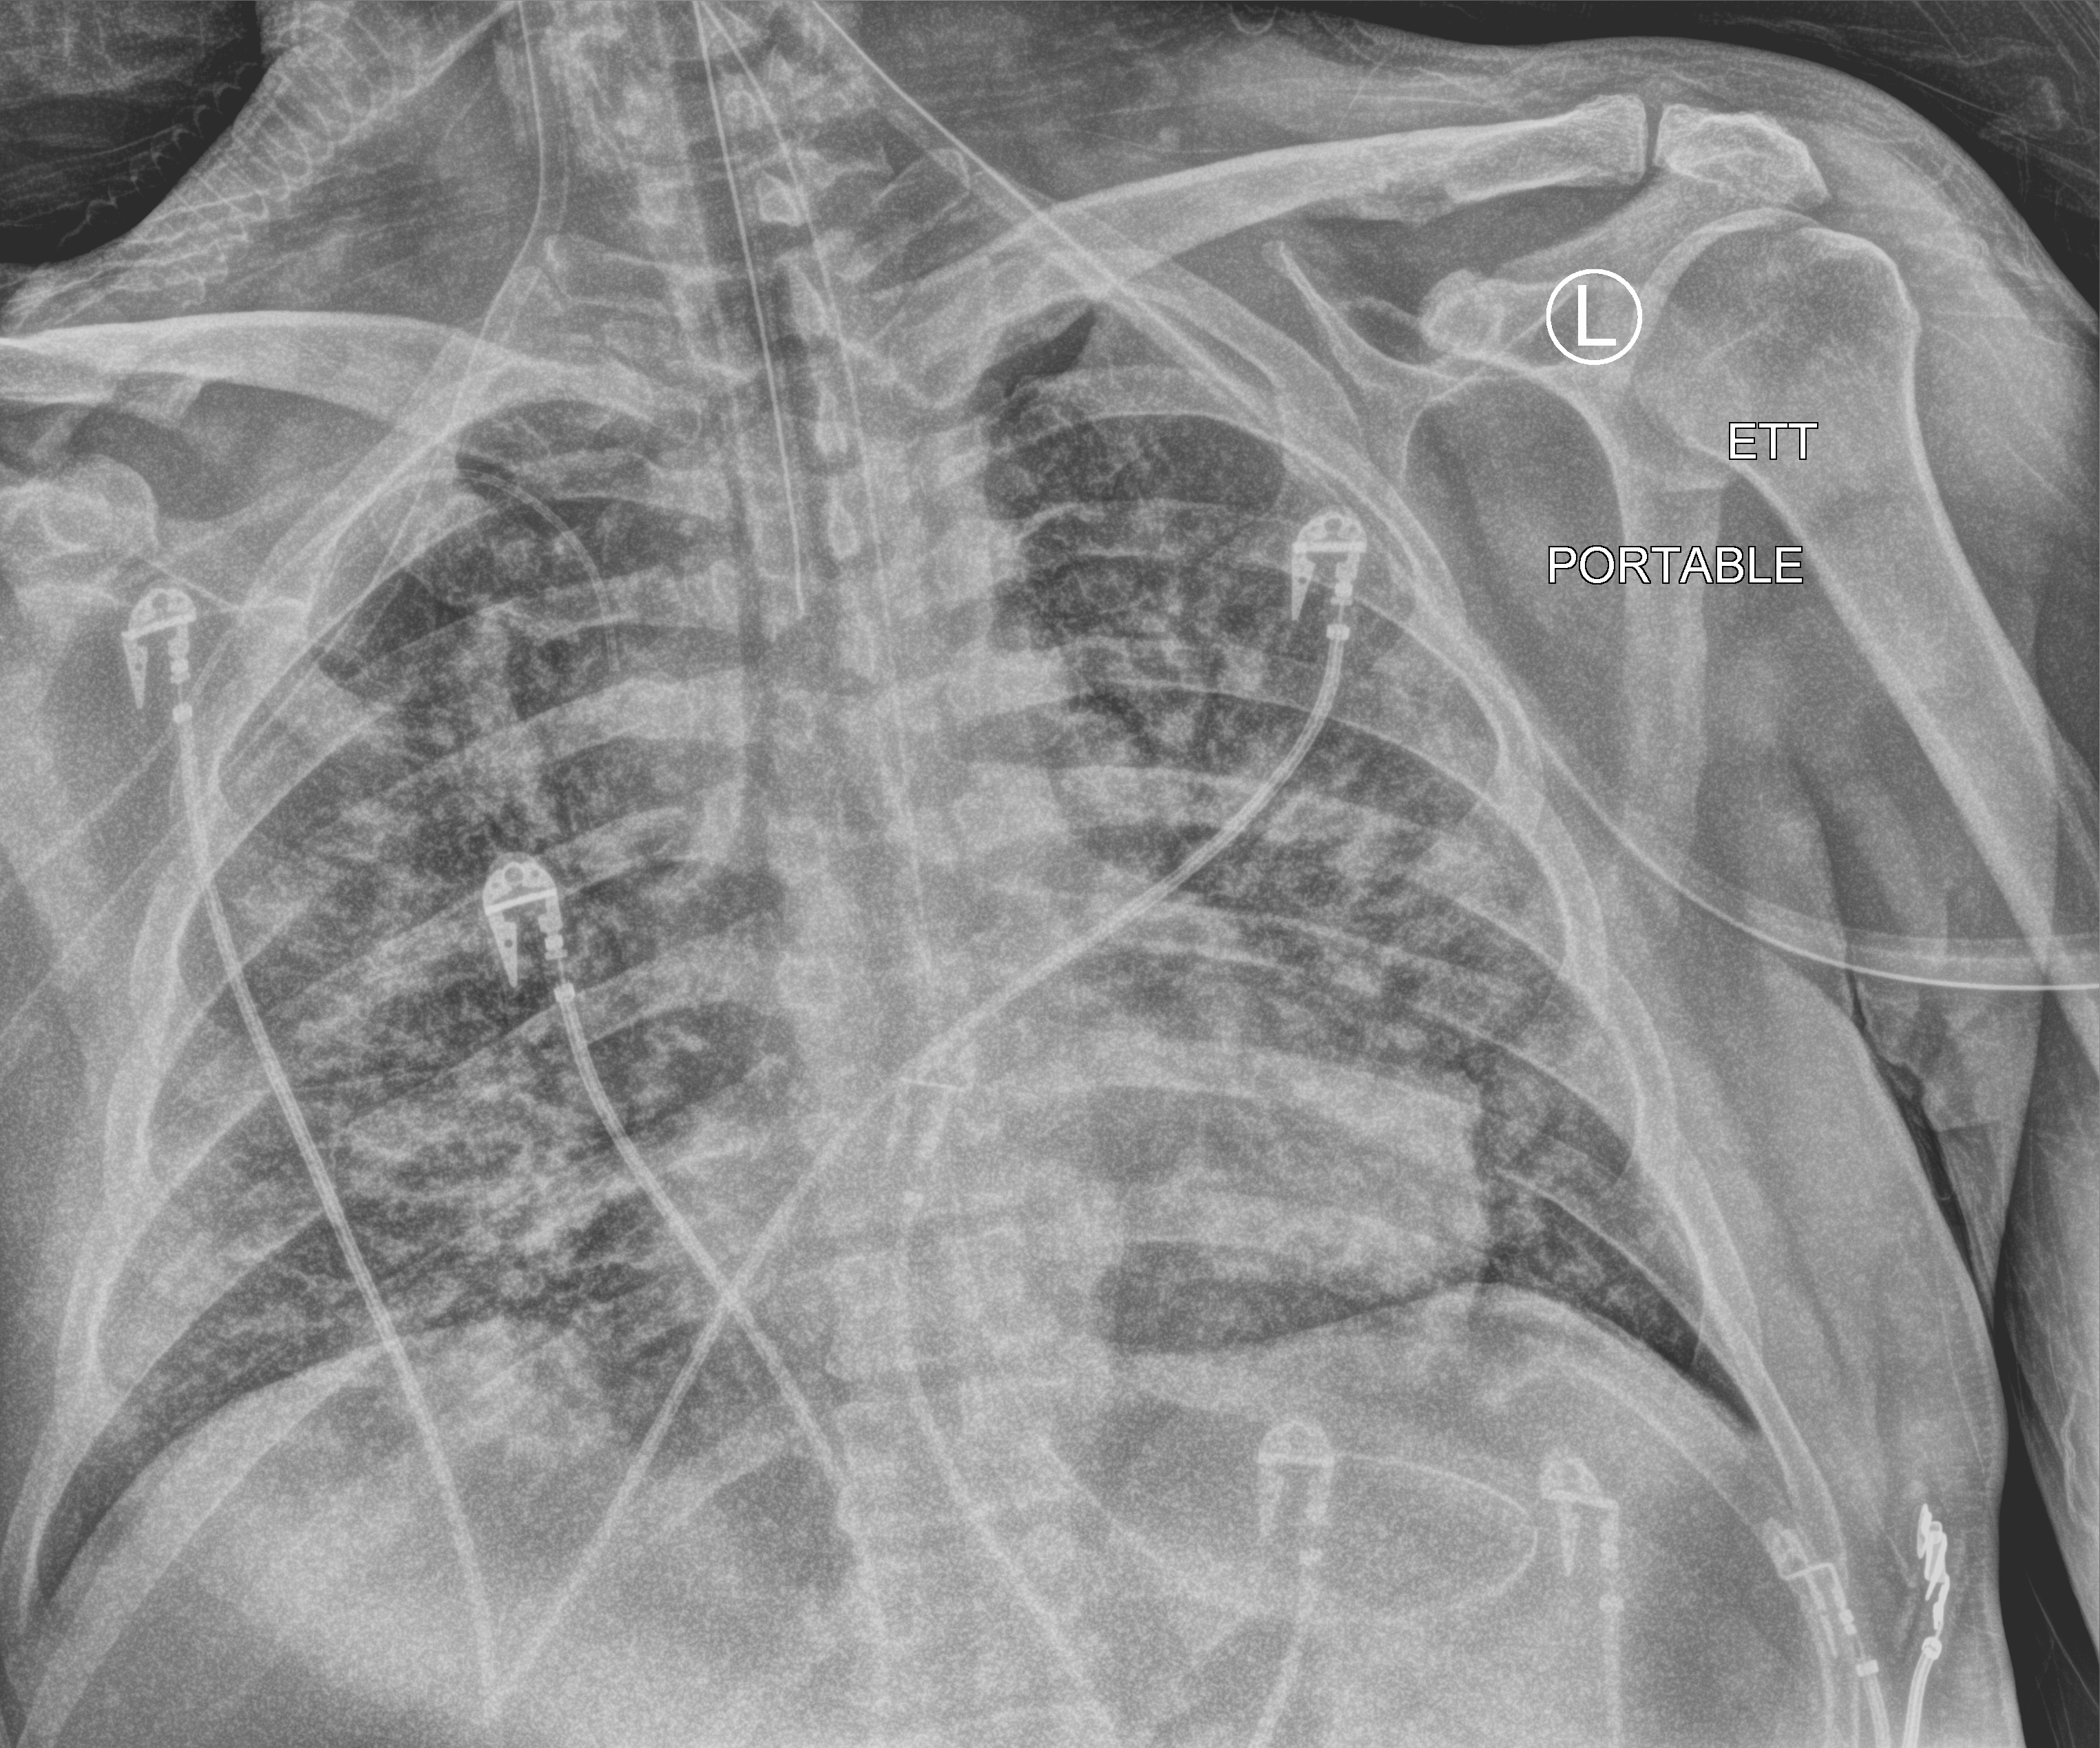
Chest X-ray (portable), anteroposterior (AP) projection. Male patient hospitalised with COVID-19, age 18–59 years.
Admission-level facts for this patient (not findings on this image; timing relative to this image not recorded): admitted to intensive care during this hospital stay: yes; other chronic lung disease (admission record): no.